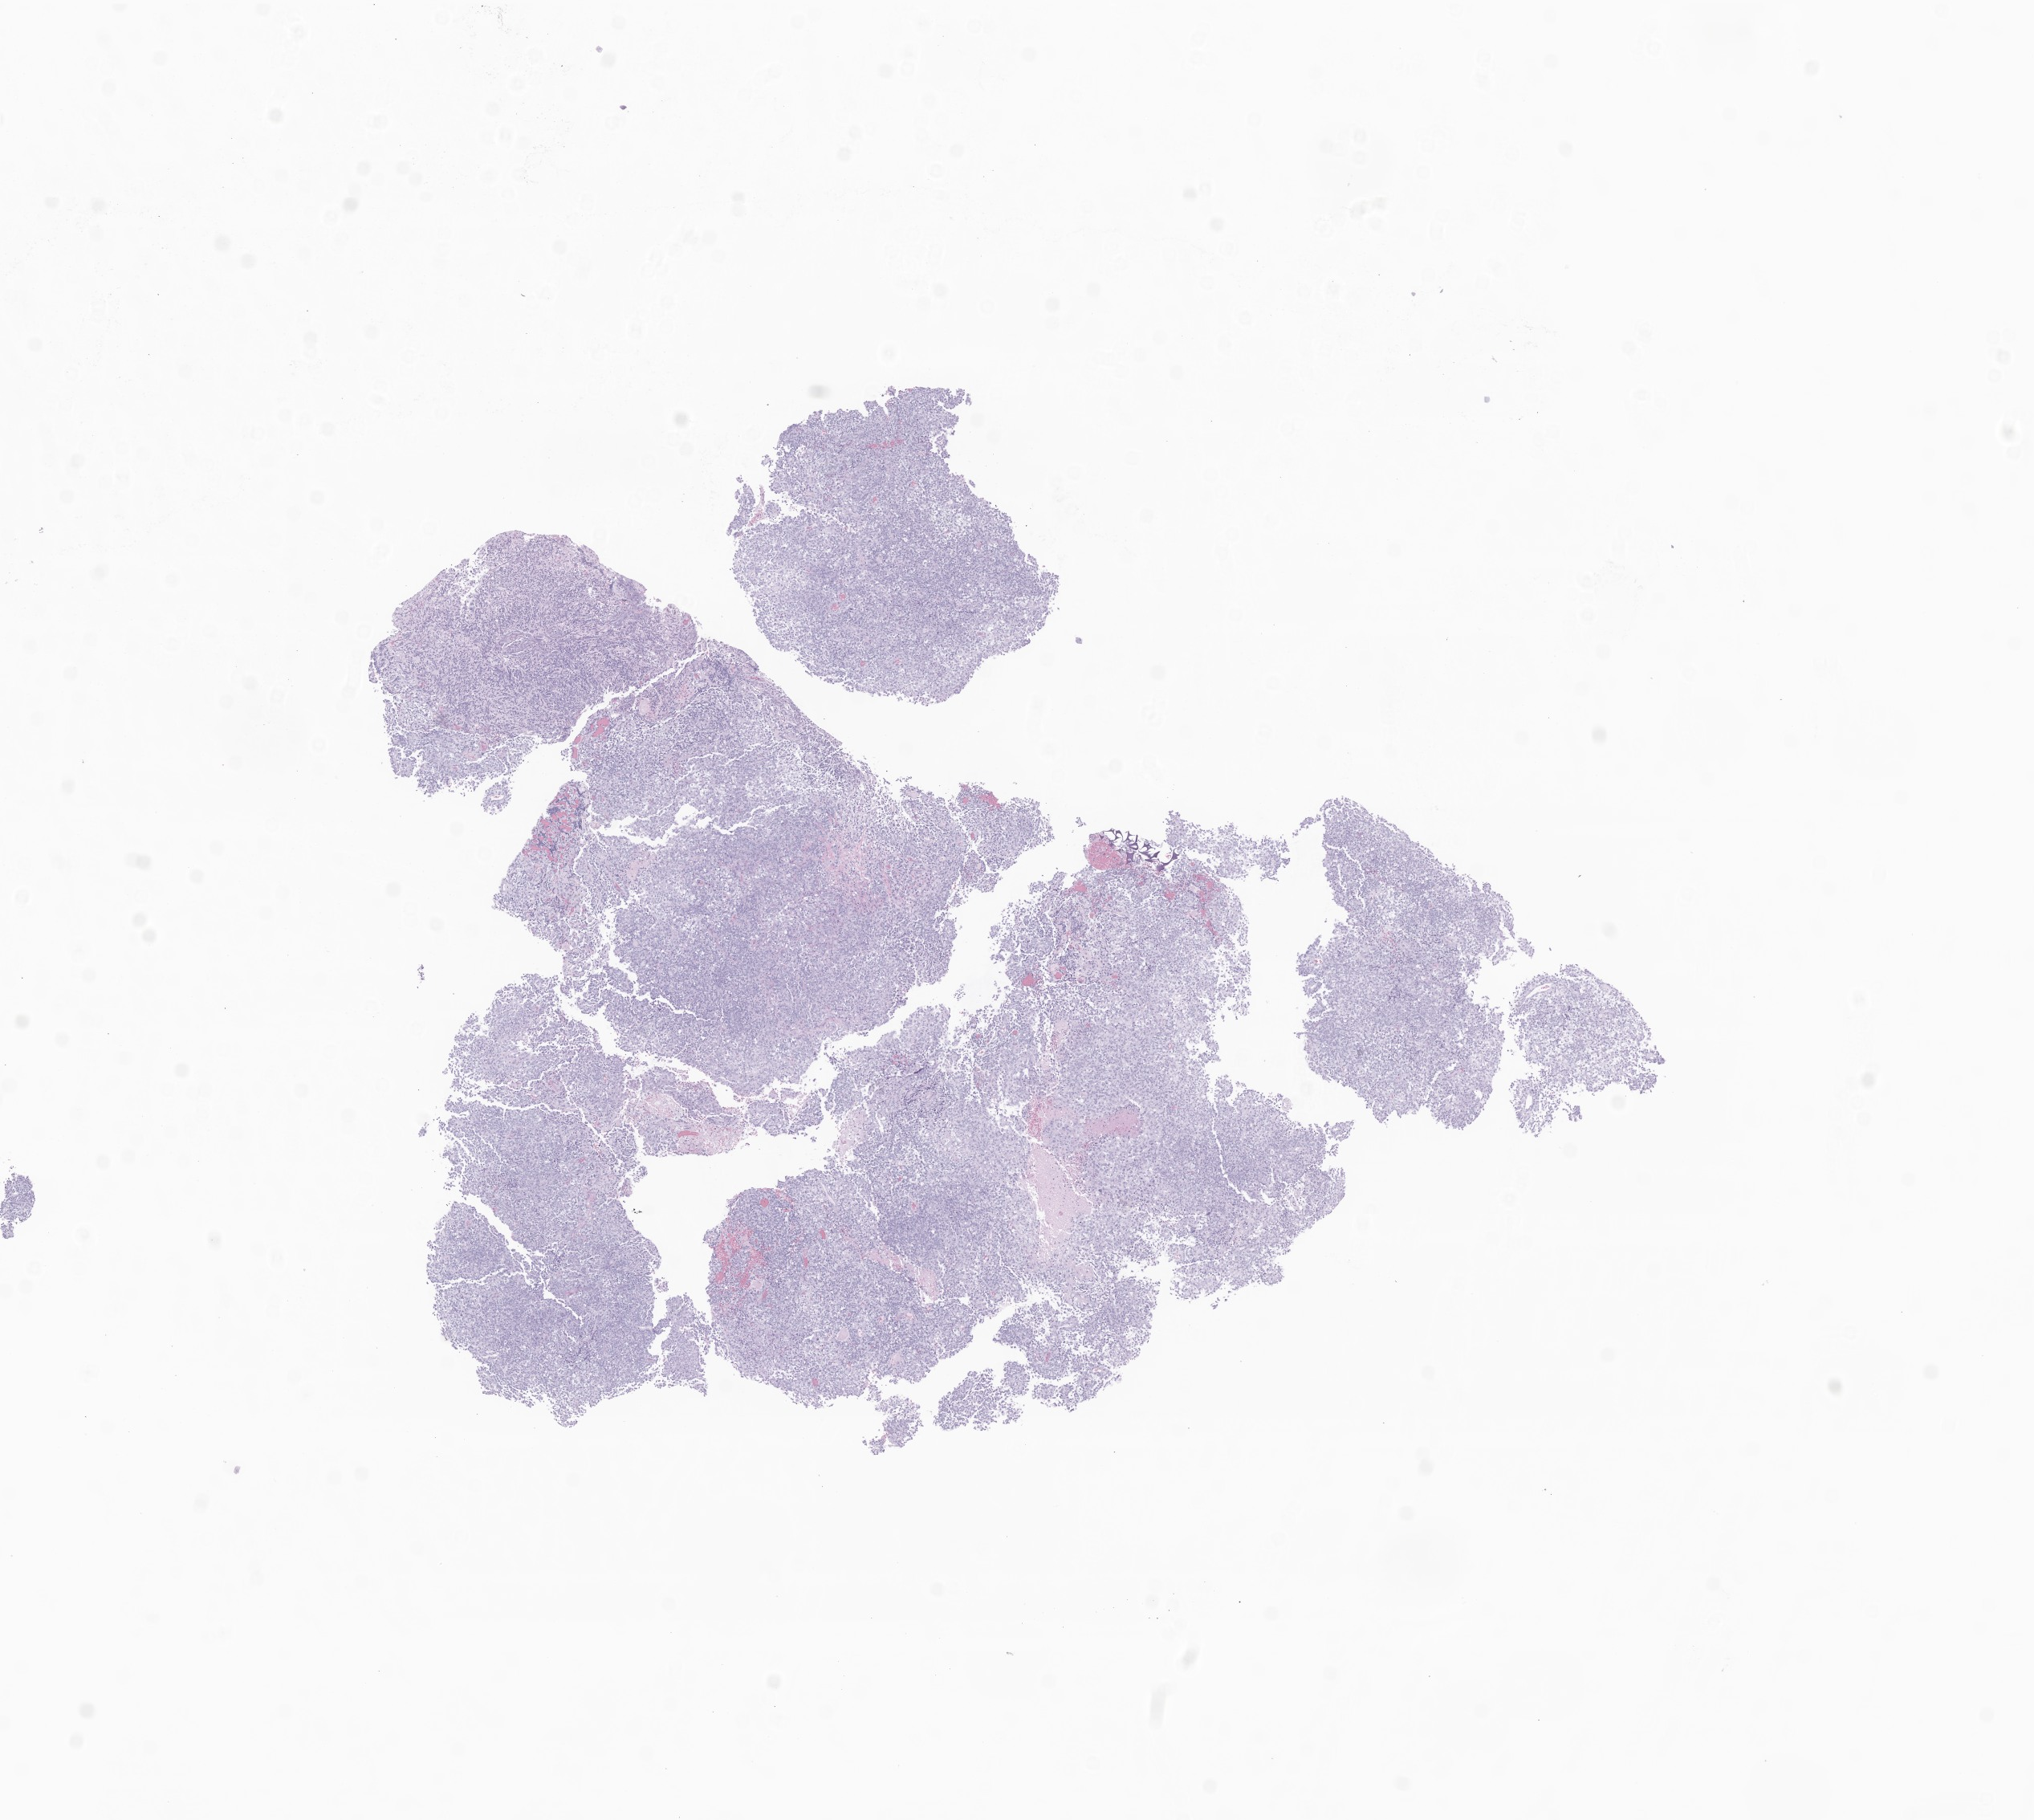
Digitized haematoxylin and eosin-stained section of tumor tissue from the brain — a low-resolution overview of the entire scanned area, about 10.7 x 9.6 mm, FFPE section. Male patient, age 311 days.
Recorded diagnosis: Atypical teratoid/rhabdoid tumor.